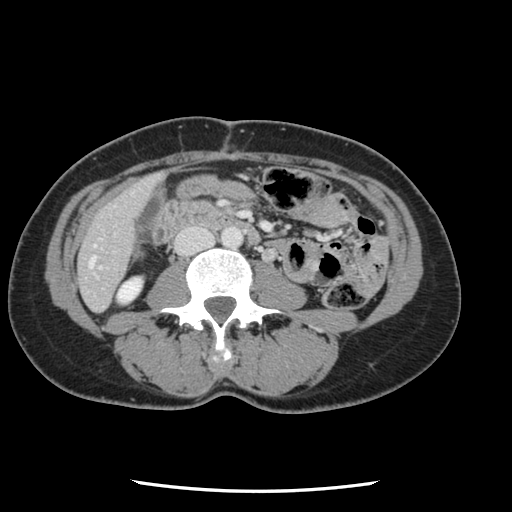
Contrast-enhanced abdominal CT, one axial slice. Position 18 of 134 along the scan axis. Soft-tissue window (W 400 / L 40 HU). 2.5 mm slice thickness. 512 × 512 image matrix, field of view 330 × 330 mm. Female patient, age 43 years. Case-level facts recorded for this patient, not image findings: diagnosis: colorectal cancer liver metastases, imaged before liver resection; multiple liver metastases: yes; largest metastasis: 3.4 cm; chemotherapy before resection: no.
Structures marked on this image (expert manual segmentation):
- hepatic veins: bounding box (x1, y1, x2, y2) in pixels: (90, 258, 94, 266)
- liver: (80, 176, 159, 311)
- planned liver remnant (the part of the liver to remain after resection): (80, 176, 159, 311)